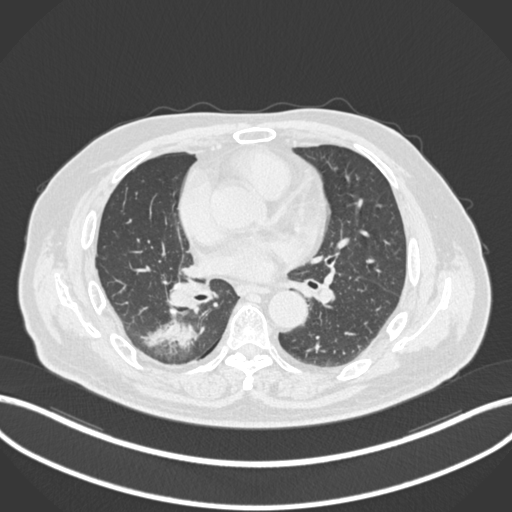
Chest CT, one axial slice; position 92 of 218 along the scan axis; reconstruction kernel B30f; 120 kVp; lung window (W 1500 / L -600 HU); 1 mm slice thickness; 512 × 512 image matrix, field of view 400 × 400 mm. Patient: male, 68 years. From the clinical record (not read from this slice): clinical TNM (as recorded): T2a N0 M0.
Outlined on this slice (bounding box drawn by a radiologist):
- lung tumour (recorded histology: adenocarcinoma): box from (x=142, y=313) to (x=198, y=358) px